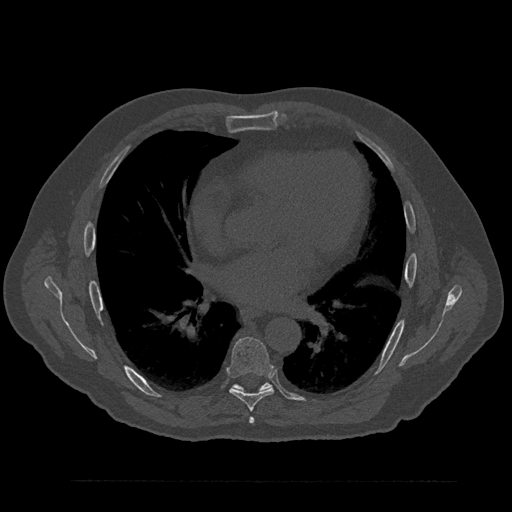
CT including the spine, one axial slice. Slice 494 of 797 in the series (ordered by position). 120 kVp. Bone window (W 1800 / L 400 HU). 512 × 512 image matrix, field of view 430 × 430 mm. Patient: male, 61 years. From the clinical record (not read from this slice): primary cancer: prostate.
Outlined on this slice (semi-automatic segmentation, software-assisted and operator-edited):
- T6 vertebra: bounding box <249,417,255,424> (left, top, right, bottom; pixels)
- T7 vertebra: <228,337,274,412>
- T8 vertebra: <233,383,272,392>